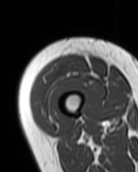
MRI of an extremity soft-tissue mass, one axial slice; slice 18 of 99 in the series (ordered by position); MR volume resampled by the dataset authors to the PET/CT grid (not the native acquisition matrix); 3.27 mm slice thickness; 138 × 172 image matrix. Female patient. From the clinical record (not read from this slice): histological type: pleiomorphic undifferentiated sarcoma; grade: high; site of the primary tumour: right quadricep.
Structures marked on this image (expert contour drawn on MRI and transferred to this co-registered scan by the dataset authors):
- gross tumour volume including surrounding oedema: bounding box [x1, y1, x2, y2] px = [32, 55, 86, 119]